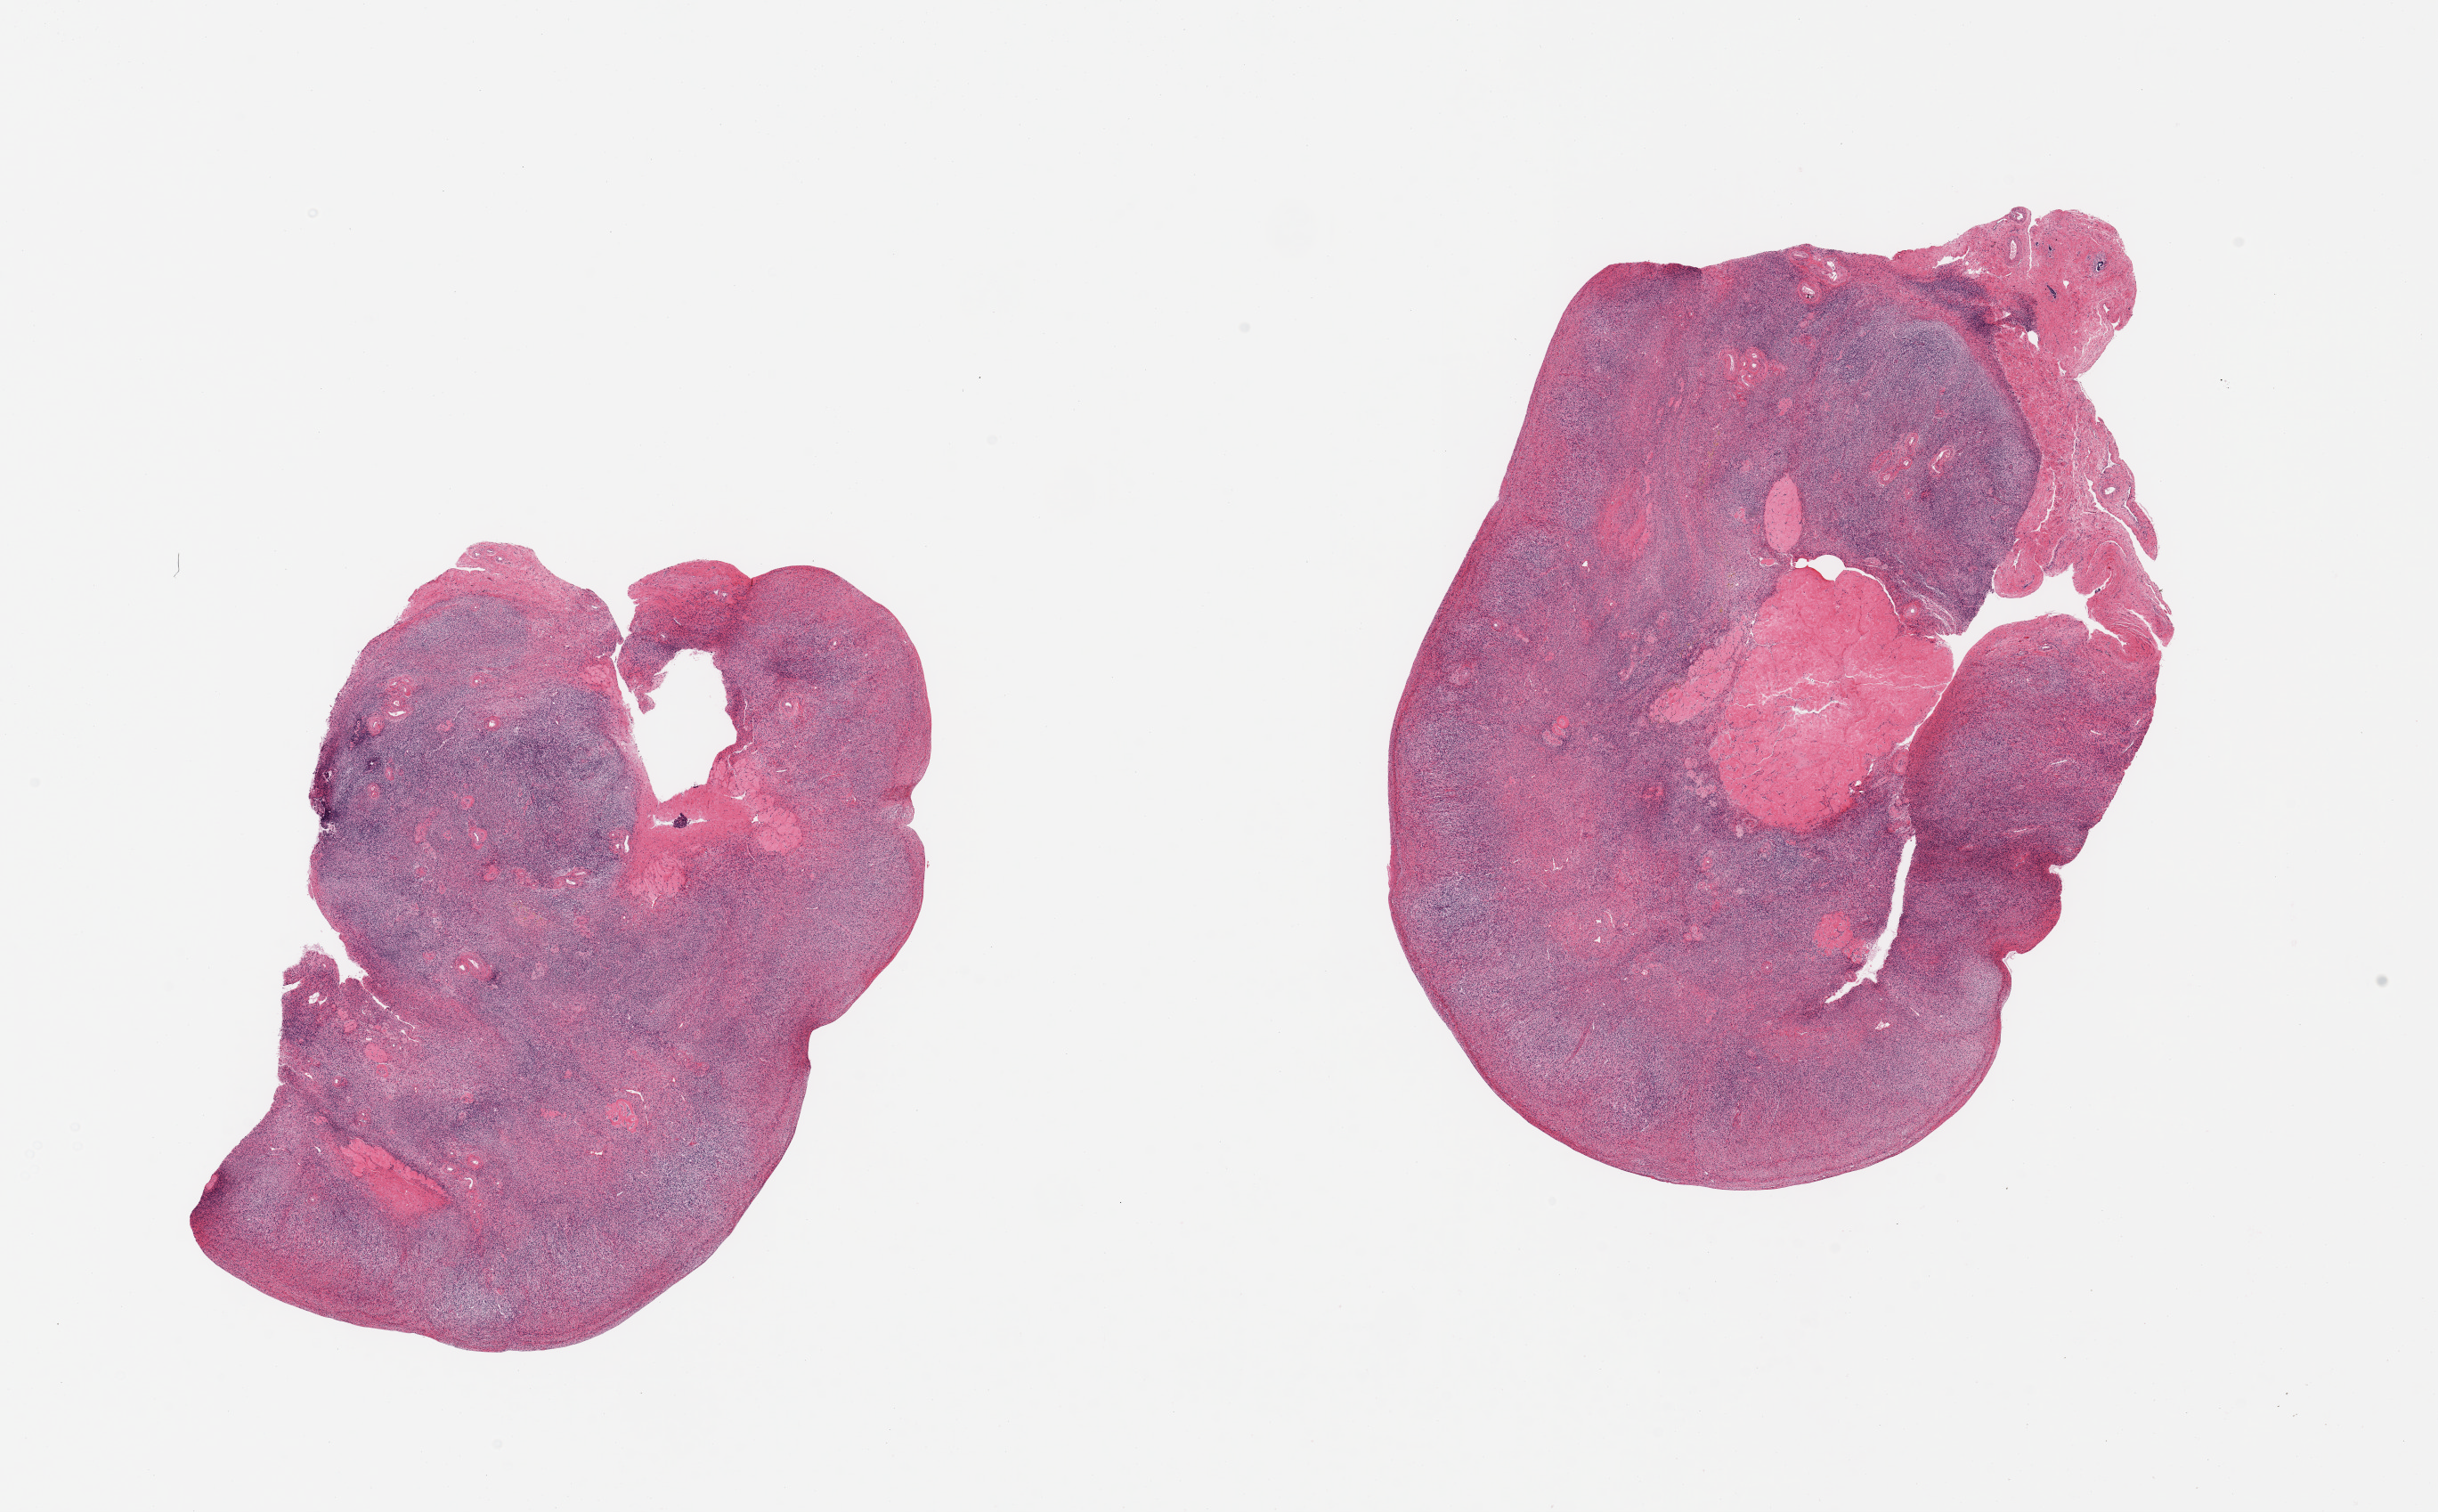
H&E whole-slide image, shown as a low-resolution overview of the whole scanned area (about 21.7 x 13.4 mm, from a 20x scan). PAXgene-fixed paraffin-embedded (PFPE) section. Section of ovary (target tissue). Donor tissue sample. Female donor.
Review note (as recorded): 2 pieces; atrophic.